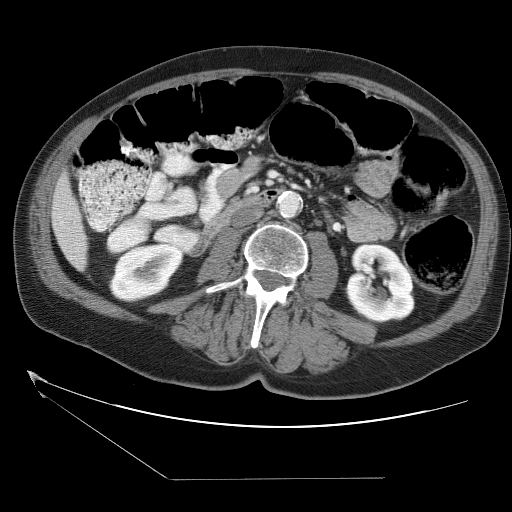
Contrast-enhanced abdominal CT (liver protocol), one axial slice; position 3 of 38 along the scan axis; 120 kVp; soft-tissue window (W 400 / L 40 HU); 5 mm slice thickness; 512 × 512 image matrix, field of view 400 × 400 mm. Case-level facts recorded for this patient, not image findings: diagnosis: hepatocellular carcinoma (patient treated with transarterial chemoembolisation; whether this scan precedes or follows treatment is not stated here); TNM stage (as recorded): Stage-II; Child-Pugh class: A; tumour differentiation: moderately differentiated; tumour nodularity: multinodular.
Outlined on this slice (semi-automatically segmented with operator editing):
- liver parenchyma outside the tumour (the mass and vessels are separate outlines, so this box may not span the whole liver): box from (x=52, y=172) to (x=86, y=270) px
- liver vessels: (x=61, y=221)–(x=63, y=224)